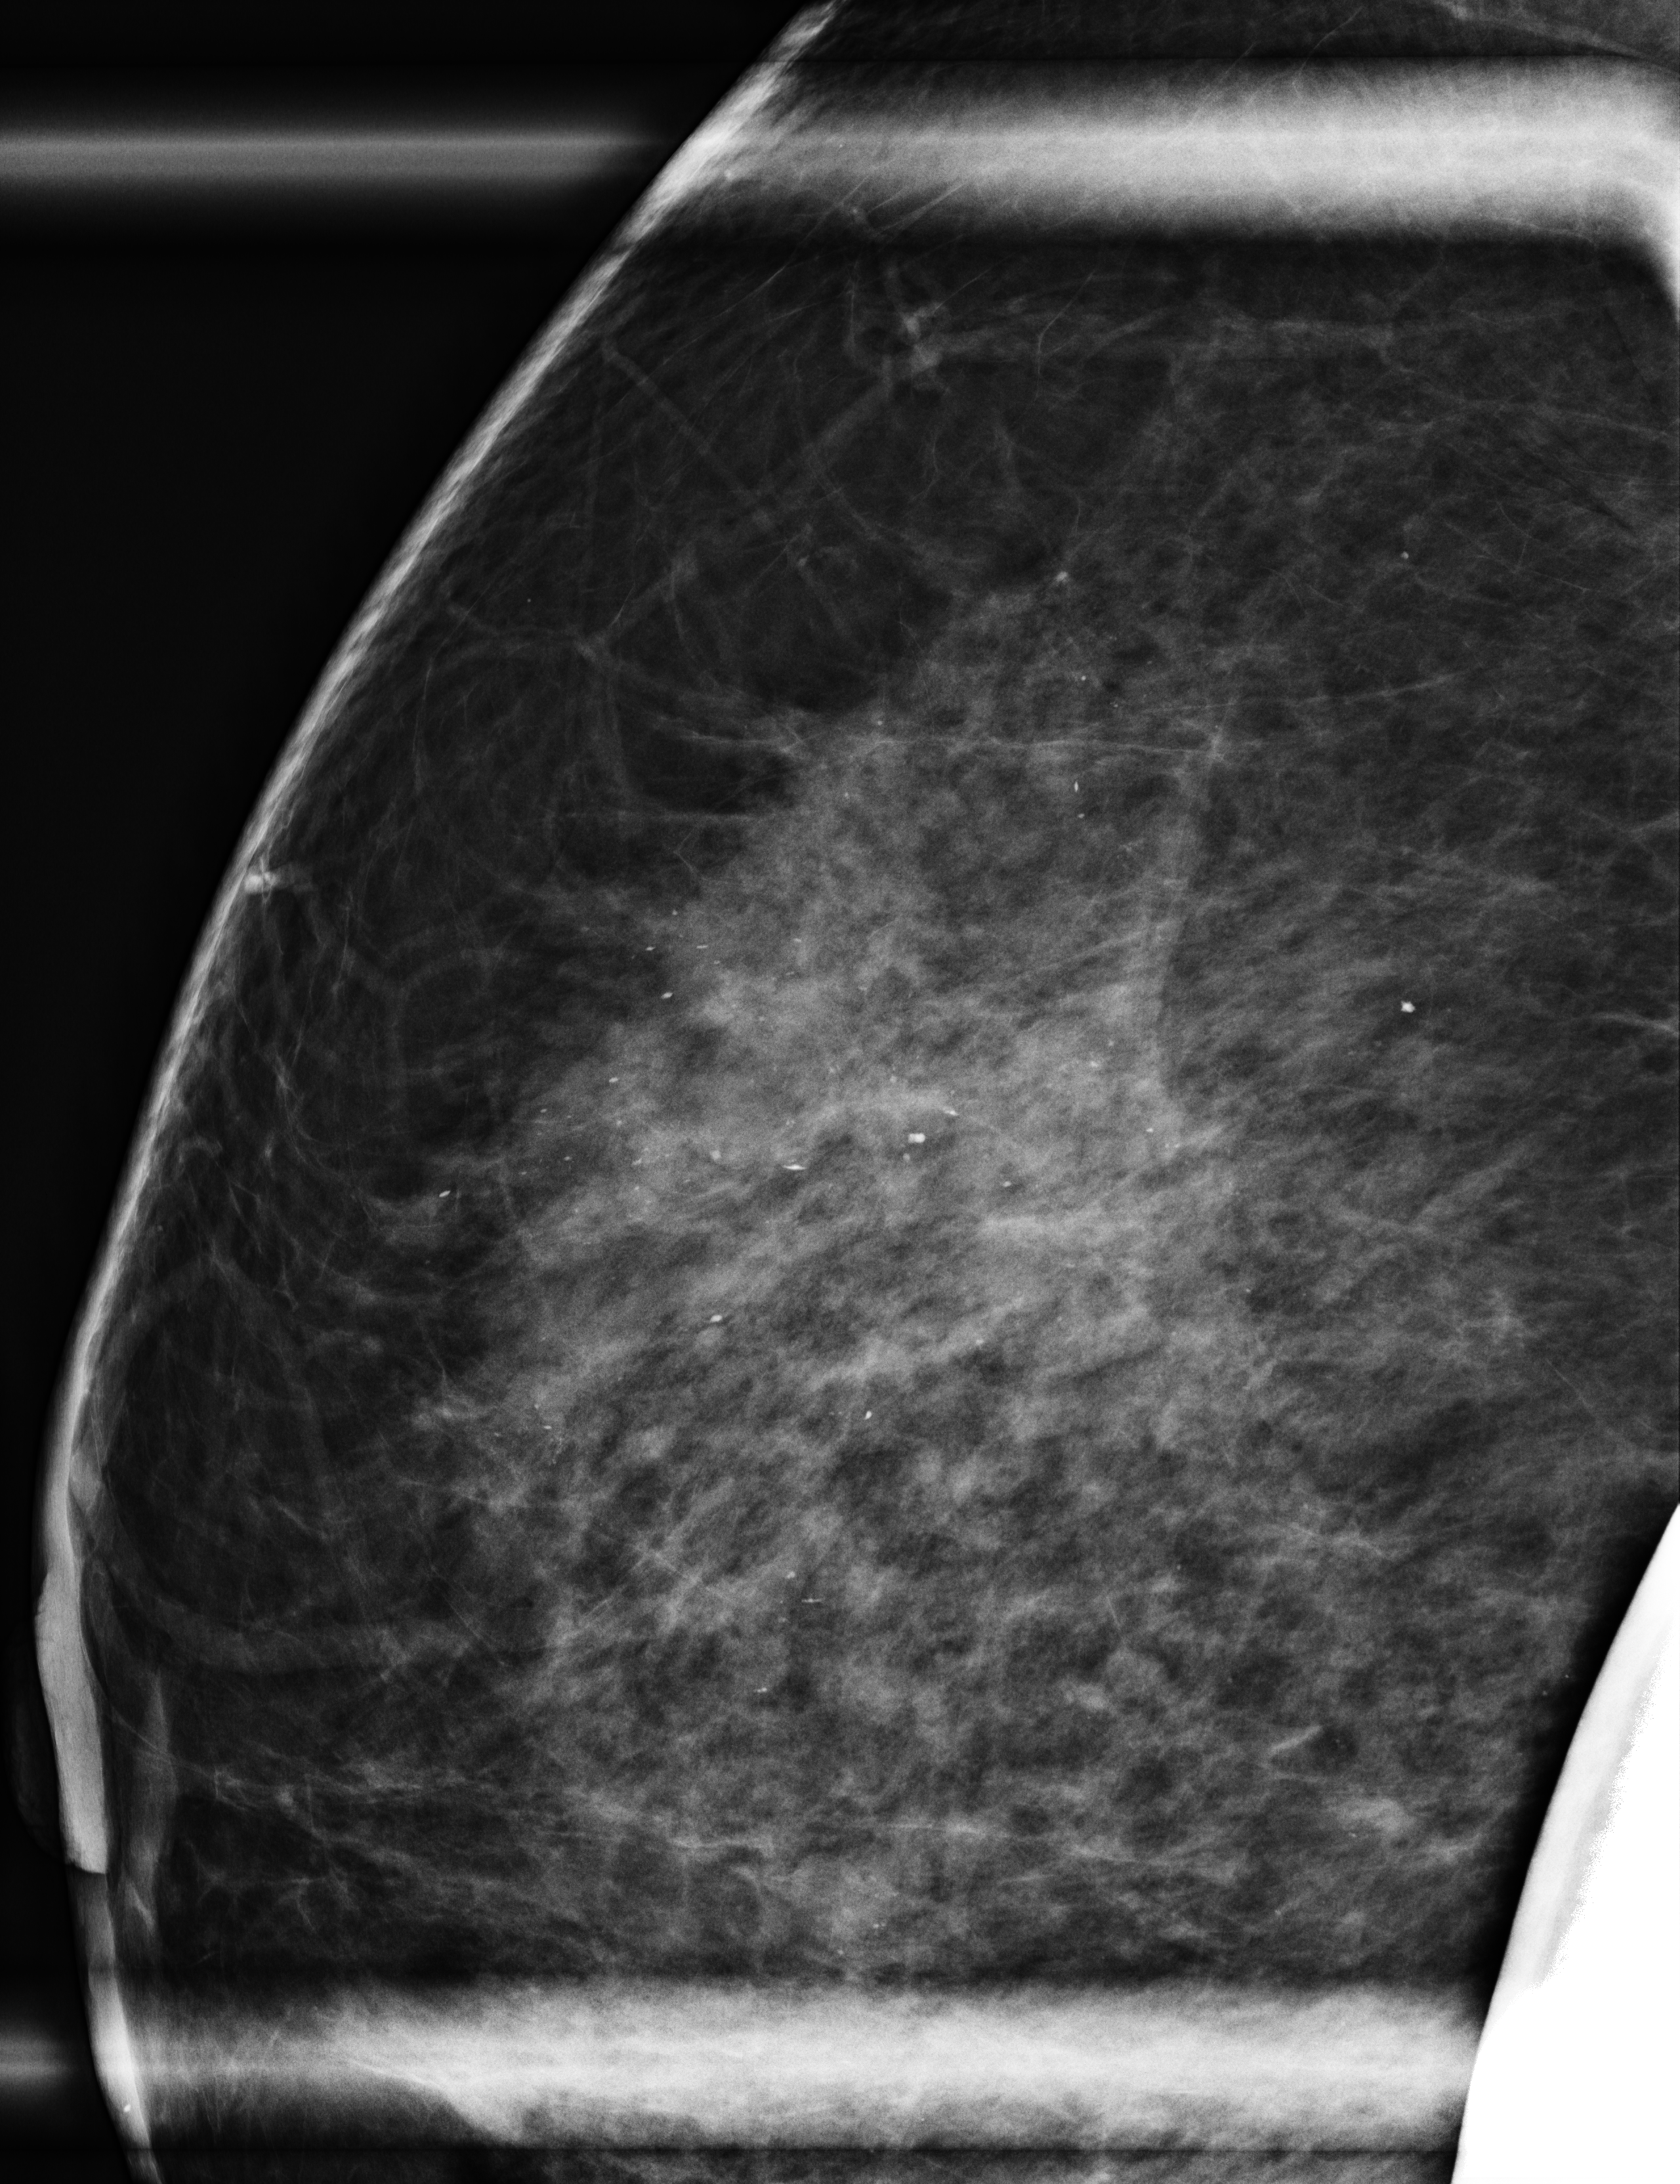
Full-field digital mammogram (FFDM), right breast, mediolateral (ML) view (magnification), additional (diagnostic) view. Female patient, age 71 years.
- BI-RADS breast density category at the screening exam (both breasts, scale 1–4): 3
- final BI-RADS assessment for this screening round (tomosynthesis exam, both breasts): category 1
- recall: recalled for additional imaging after this screen